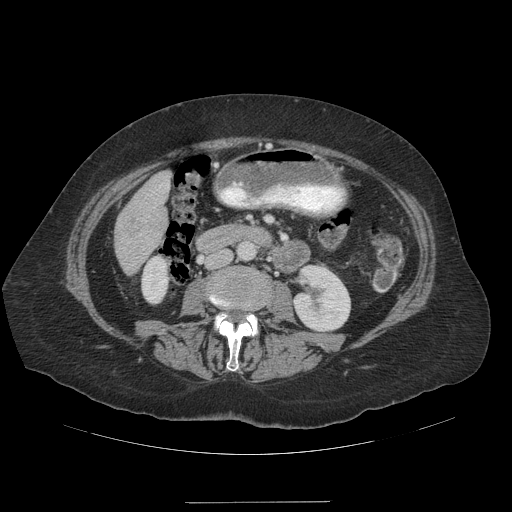
Contrast-enhanced abdominal CT (liver protocol), one axial slice; position 36 of 99 along the scan axis; 140 kVp; soft-tissue window (W 400 / L 40 HU); 2.5 mm slice thickness; 512 × 512 image matrix, field of view 440 × 440 mm. Case-level facts recorded for this patient, not image findings: diagnosis: hepatocellular carcinoma (patient treated with transarterial chemoembolisation; whether this scan precedes or follows treatment is not stated here); TNM stage (as recorded): Stage-IVA; Child-Pugh class: A; tumour nodularity: multinodular.
Annotated regions visible in this slice (semi-automatic segmentation, software-assisted and operator-edited):
- liver parenchyma outside the tumour (the mass and vessels are separate outlines, so this box may not span the whole liver): bounding box <114,172,170,274> (left, top, right, bottom; pixels)
- liver vessels: <159,183,169,188>